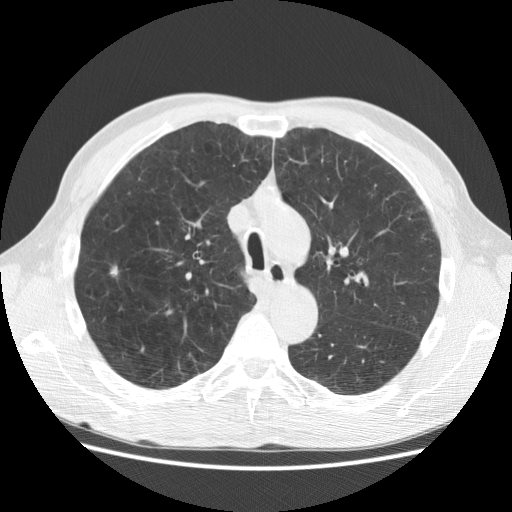
Chest CT (low-dose screening protocol), one axial image. First (baseline) screen. Lung window (W 1500 / L -600 HU). Standard (soft-tissue) reconstruction kernel (STANDARD). Male, age 62 years at enrolment. Current smoker at enrolment.
Expert-annotated lung lesion, box from (x=101, y=260) to (x=133, y=290) px. The screening reader recorded 2 non-calcified nodules or masses ≥4 mm on this exam (right upper lobe, left lower lobe); which of them this box marks is not recorded.